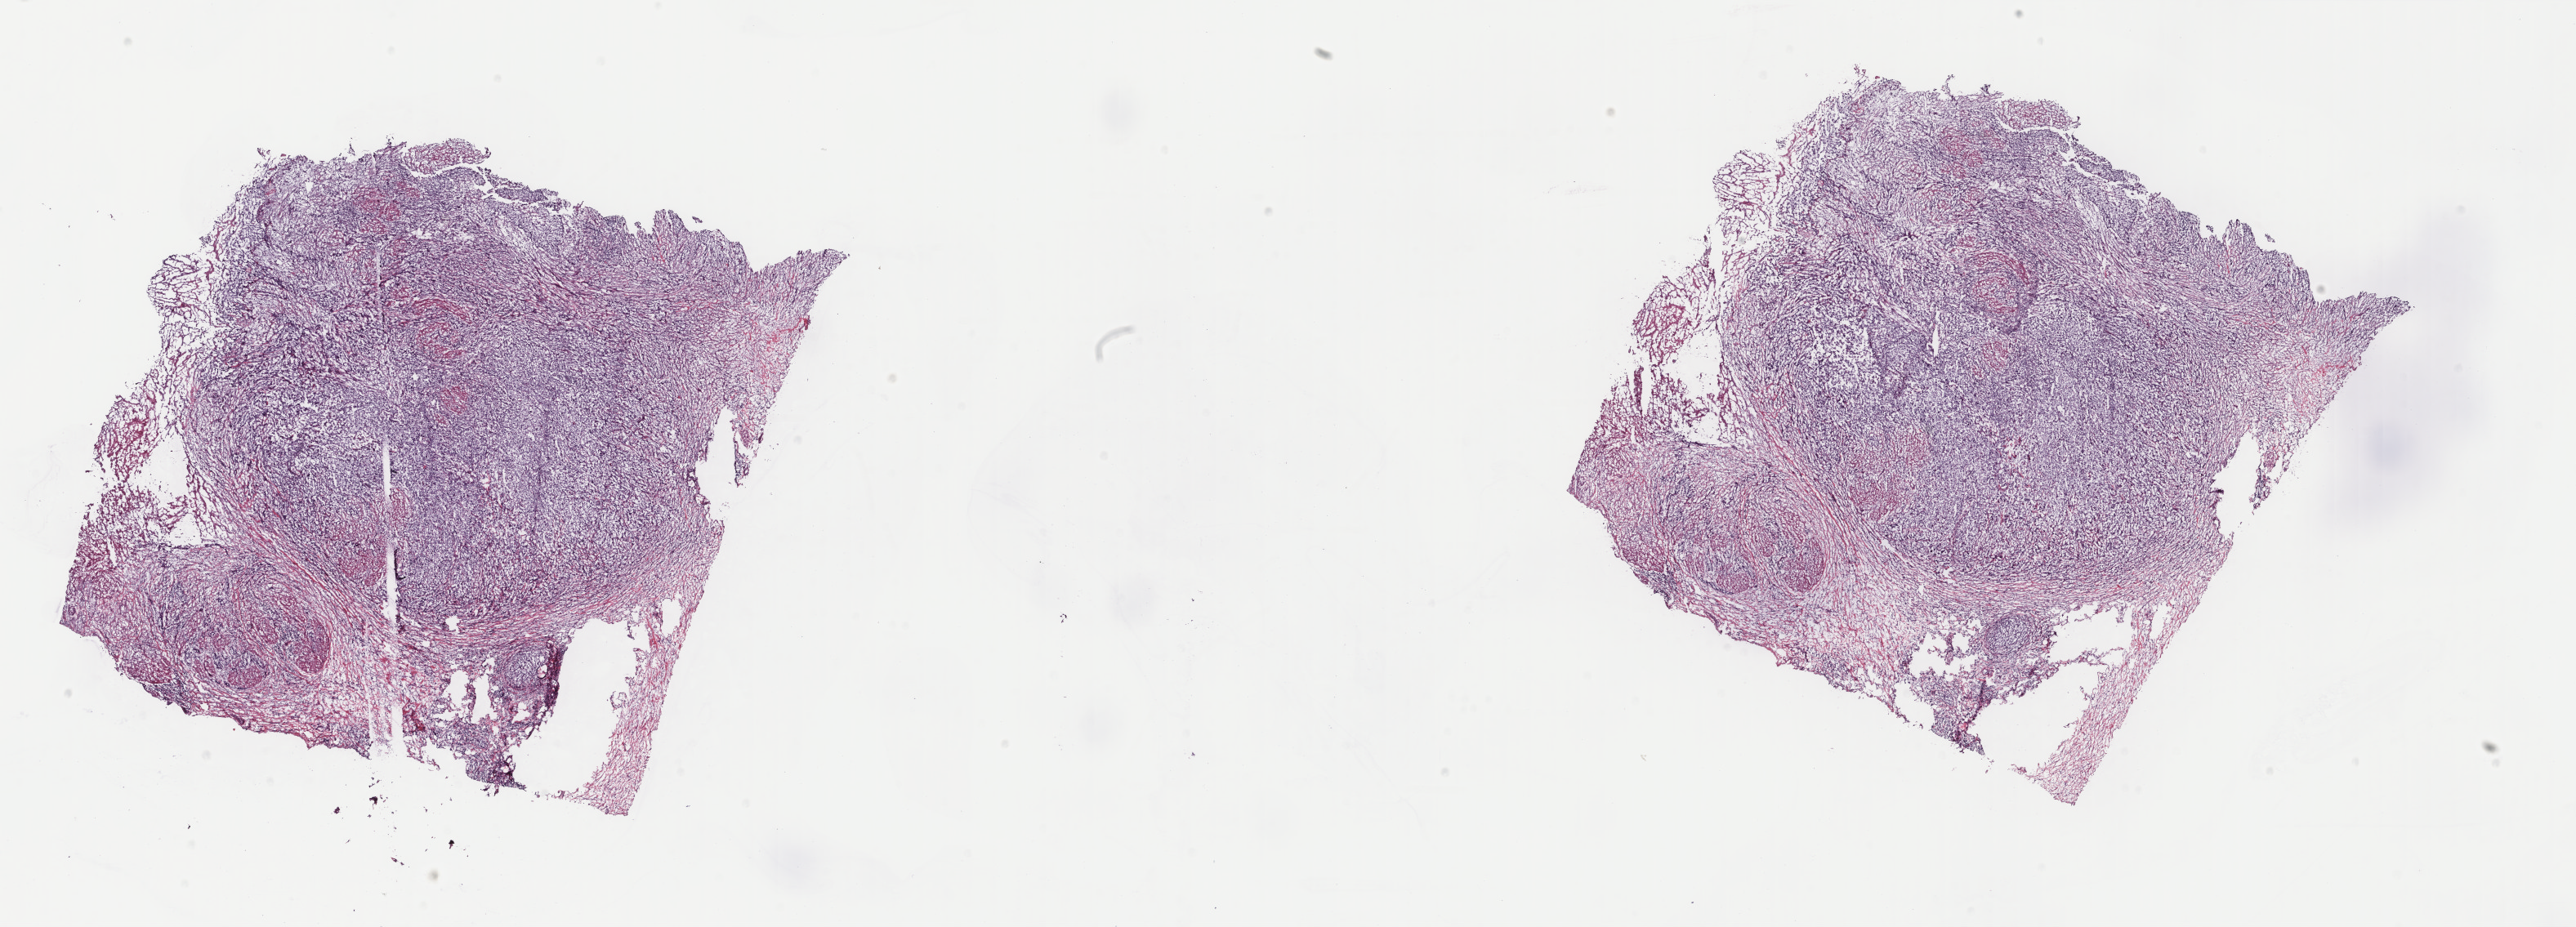
H&E-stained whole-slide image — shown as a low-resolution overview of the whole scanned area (about 25.0 x 9.0 mm). Frozen section from the top of the tissue portion. Sample: primary tumour, bladder. Female patient; age at initial diagnosis 61 years. Histologic grade: high grade. Pathologist review of this section (percent, as recorded): tumour cells 75%, tumour nuclei 75%, normal cells 0%, stromal cells 25%, necrosis 0%. Infiltration values recorded for this section: lymphocyte infiltration 6%, monocyte infiltration 2%, neutrophil infiltration 5%.
- TNM: T3b N0 MX
- AJCC pathologic stage: III (7th edition)
- pathologic diagnosis: Transitional cell carcinoma (posterior wall of bladder)
- lymph nodes positive (case pathology): 0 of 30 examined